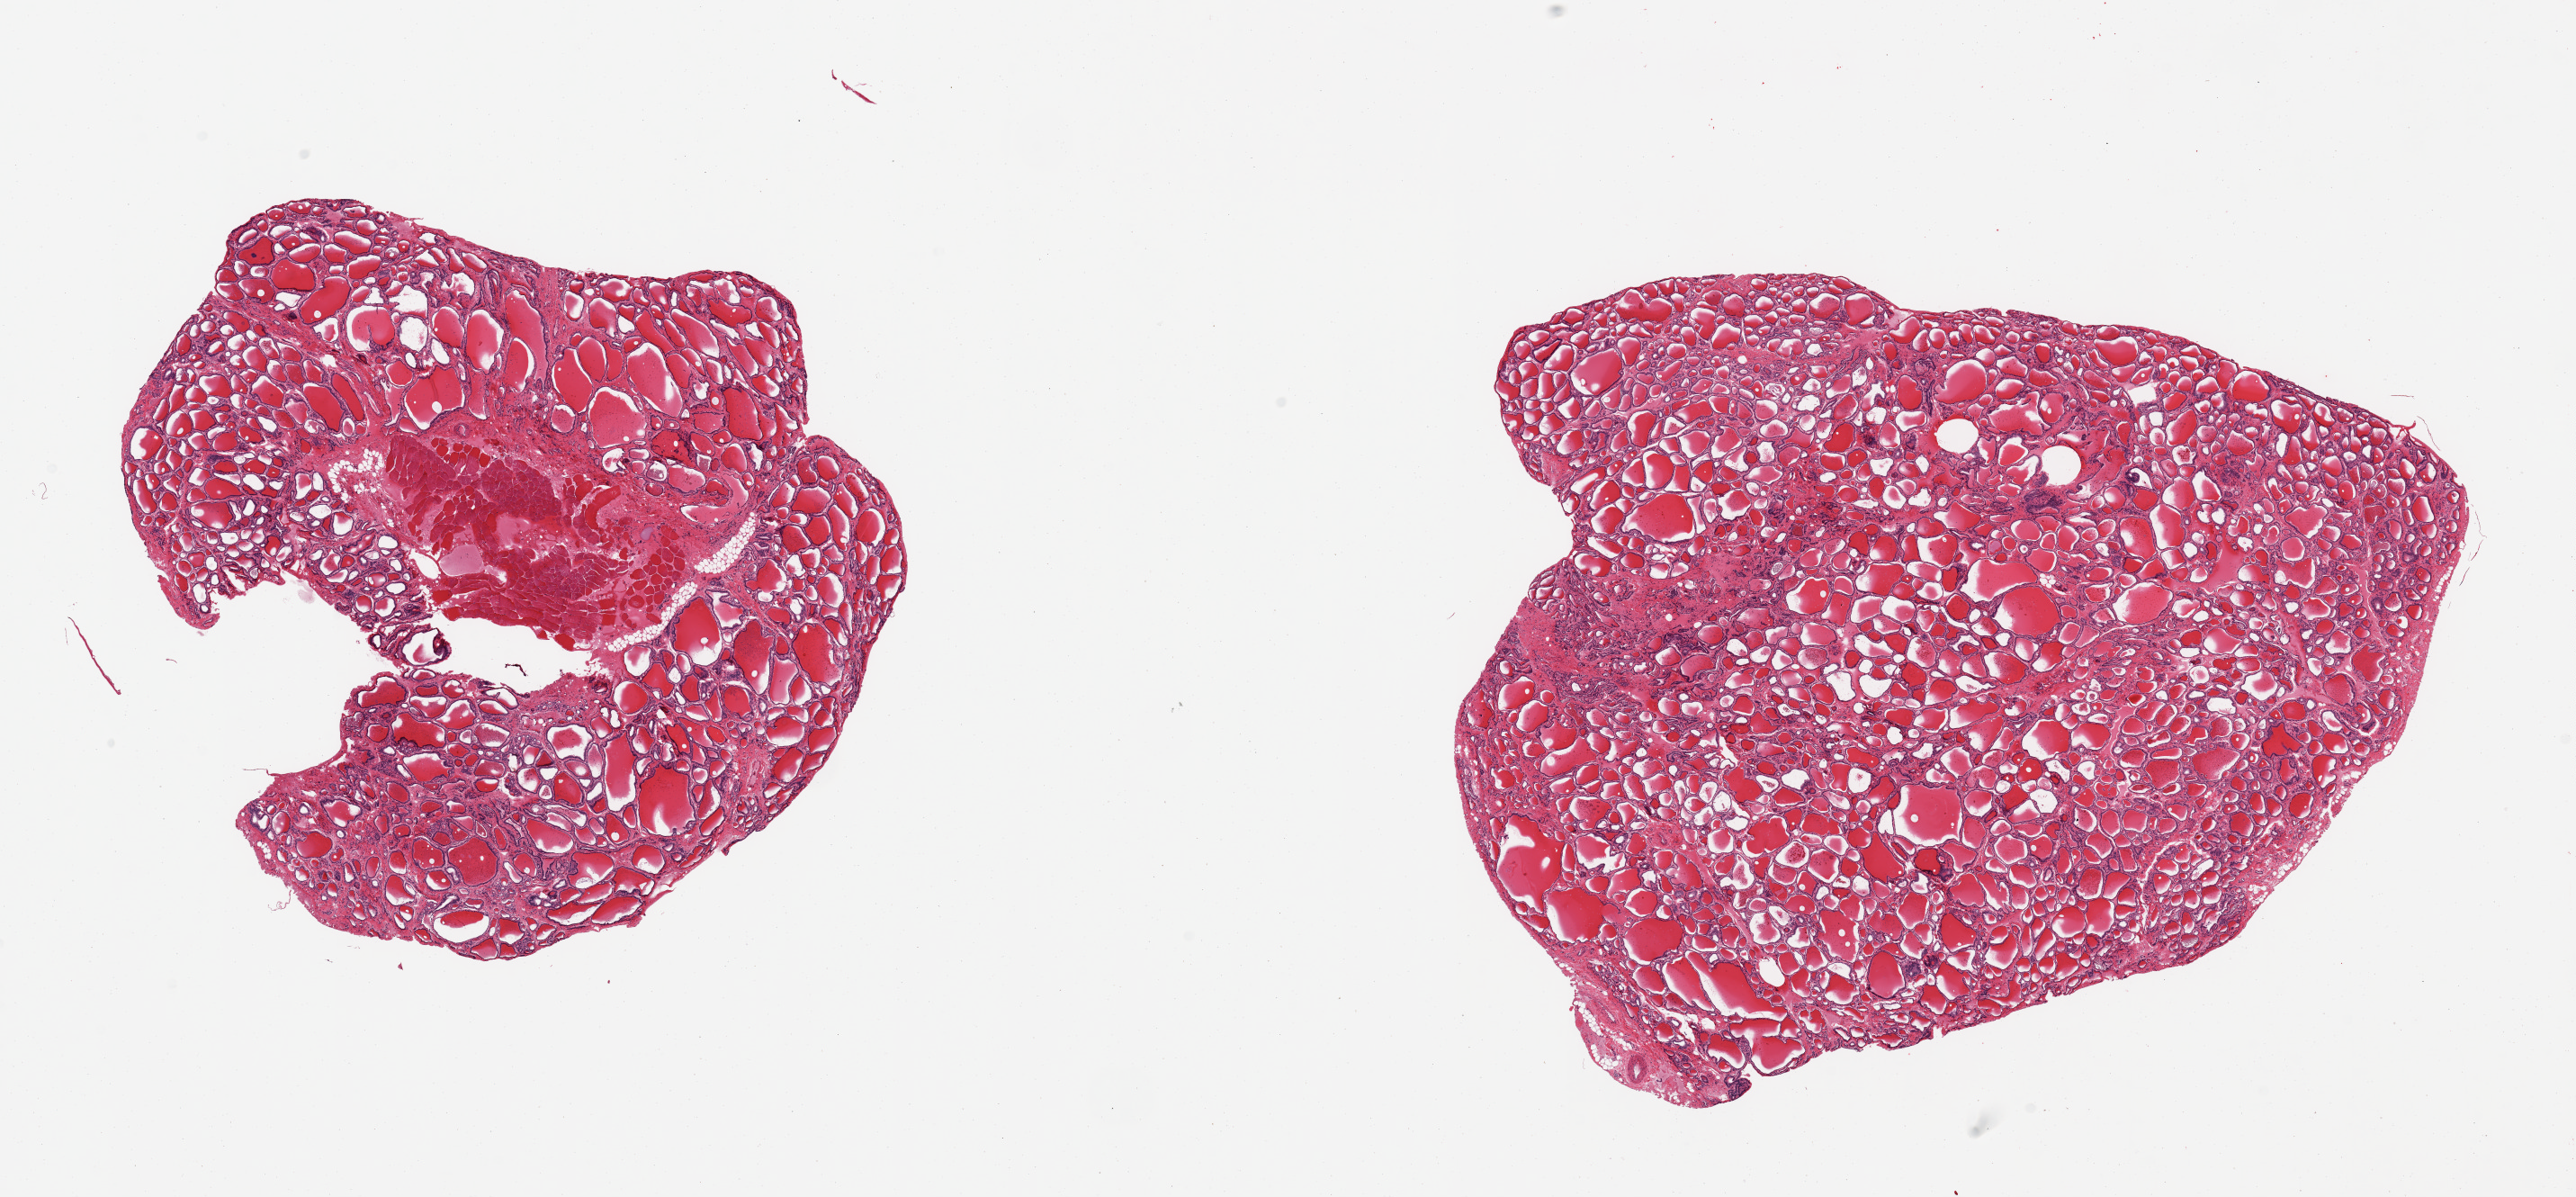
Digitized haematoxylin and eosin-stained section — a low-resolution overview of the entire scanned area, about 22.6 x 10.5 mm (acquisition: 20x scan); PAXgene-fixed paraffin-embedded (PFPE) section; section of thyroid (target tissue); tissue donor sample. Donor sex: male.
Review note (as recorded): 2 pieces; 2.5mm centyral focus of skeletal muscle.